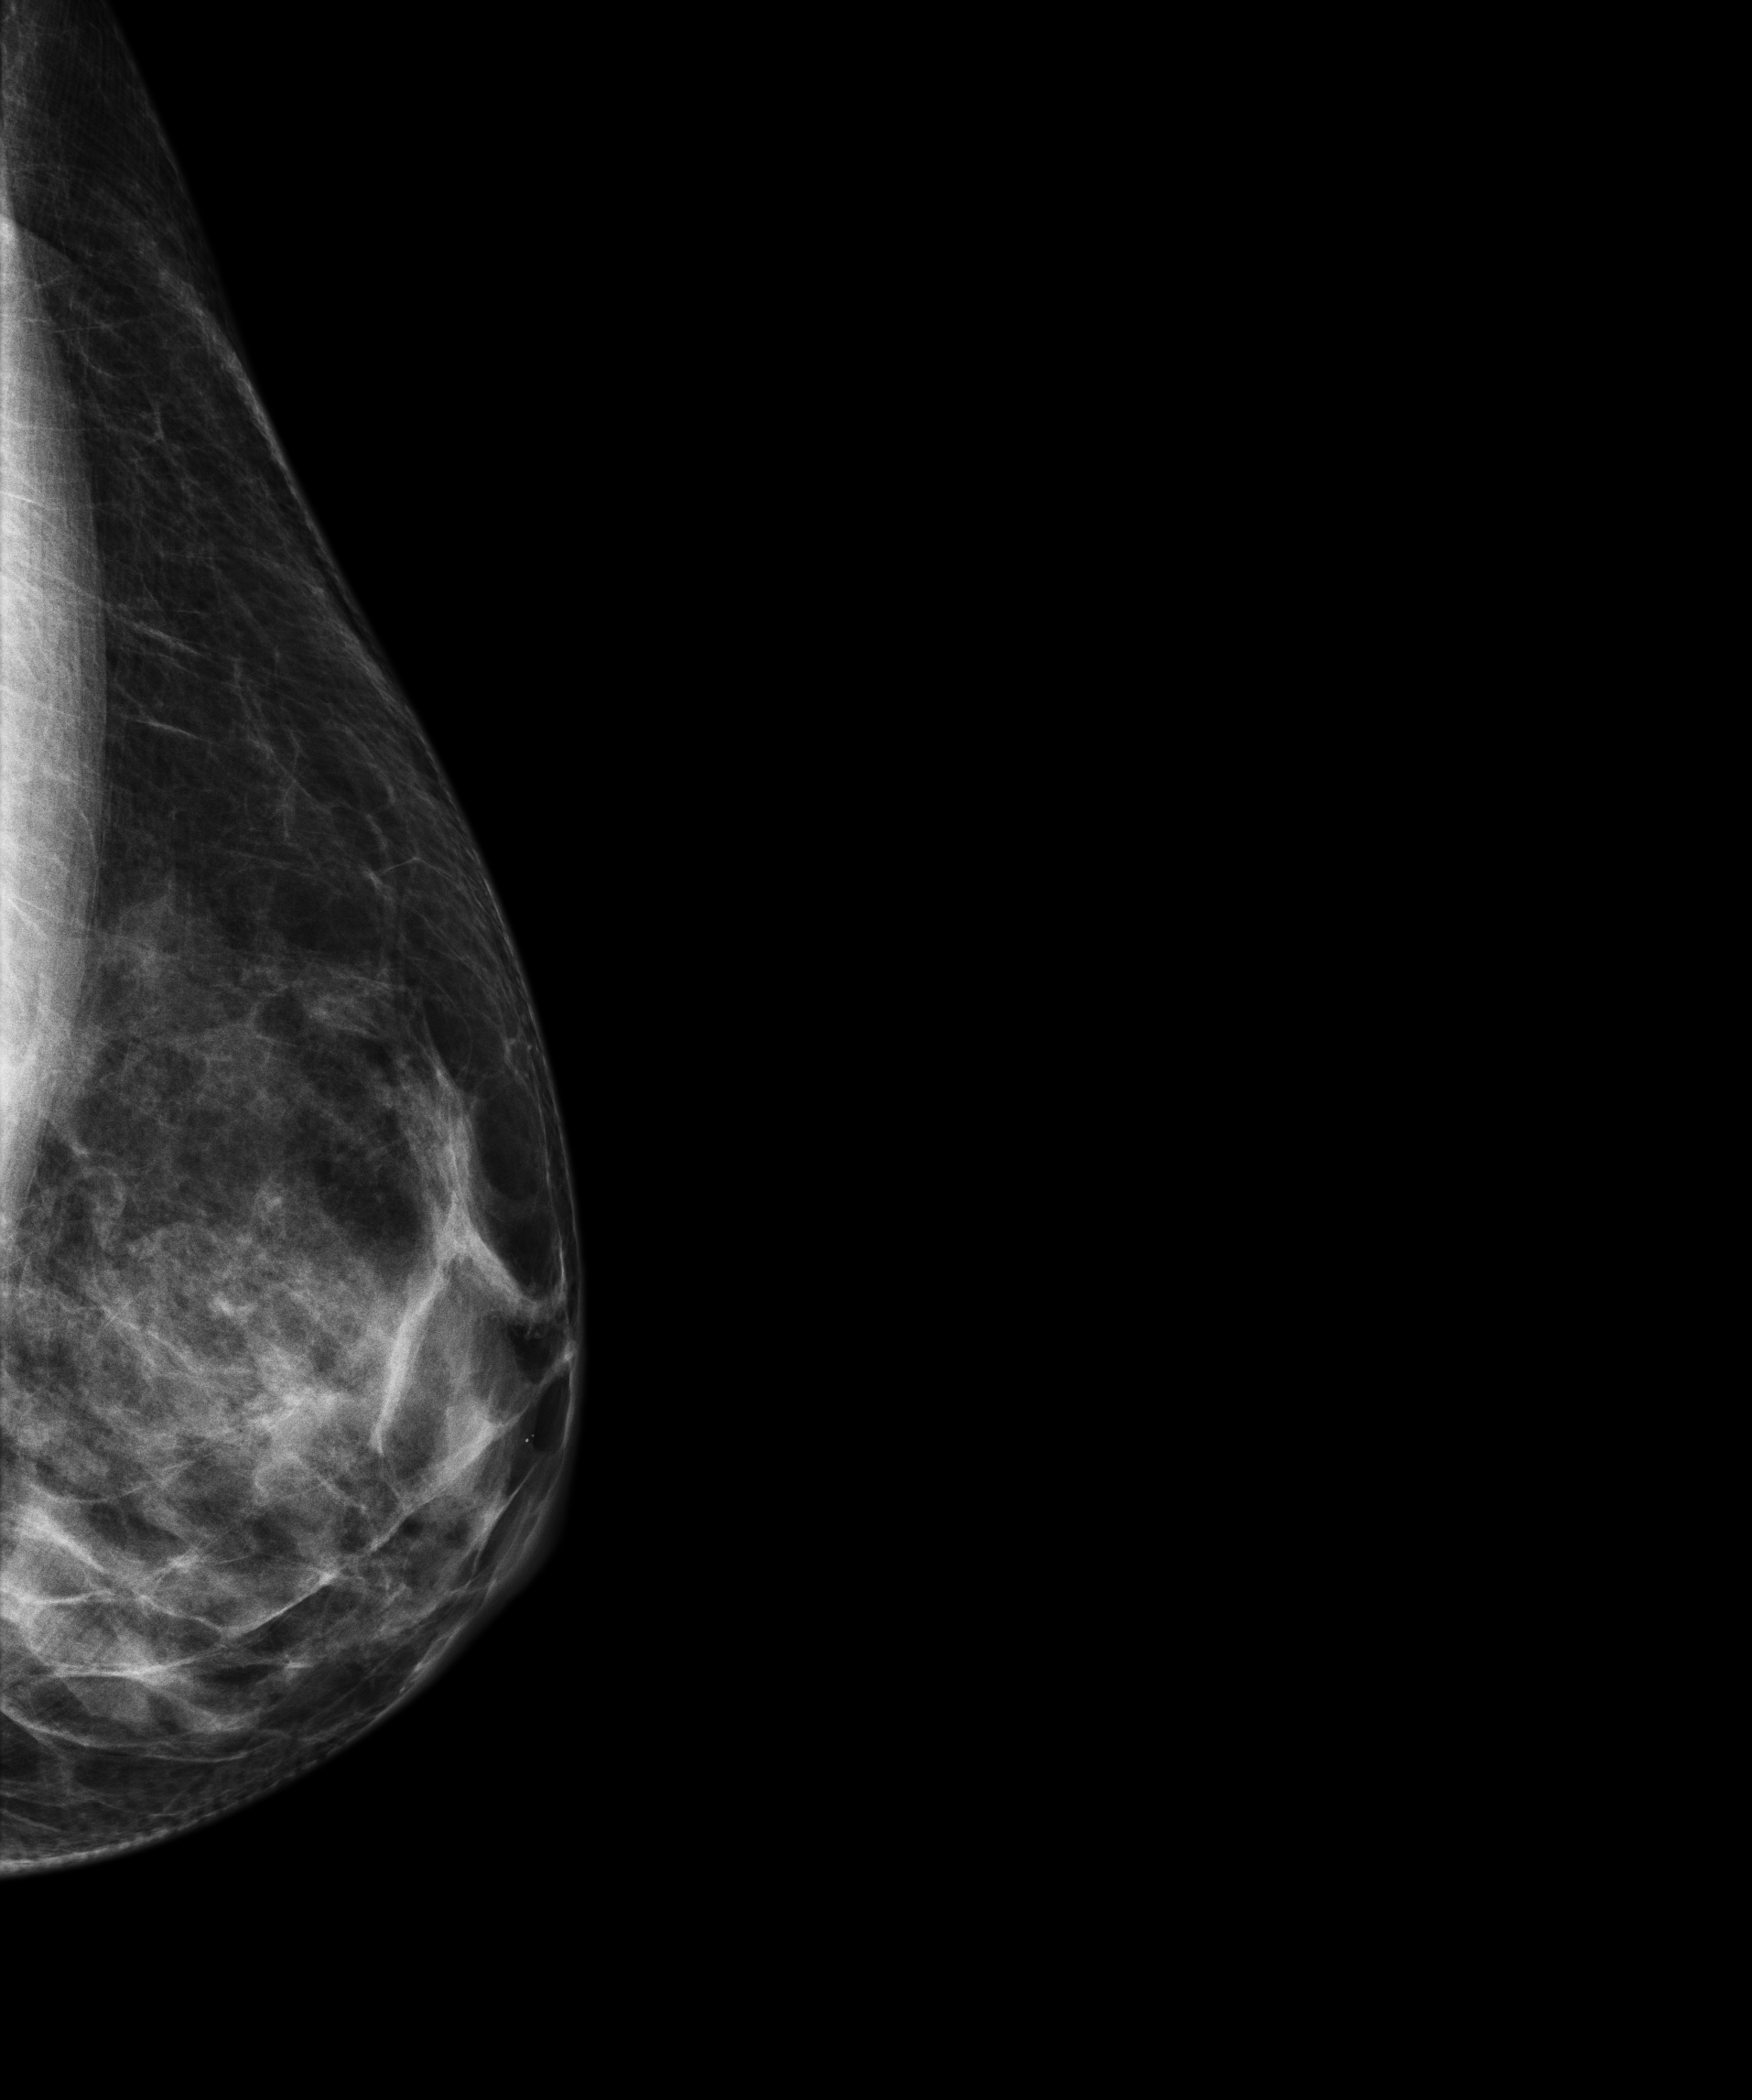
Annual screening mammography examination. Female patient, age 67 years.
Image type: full-field digital mammogram. Breast: left. Projection: laterally exaggerated craniocaudal (XCCL) view.